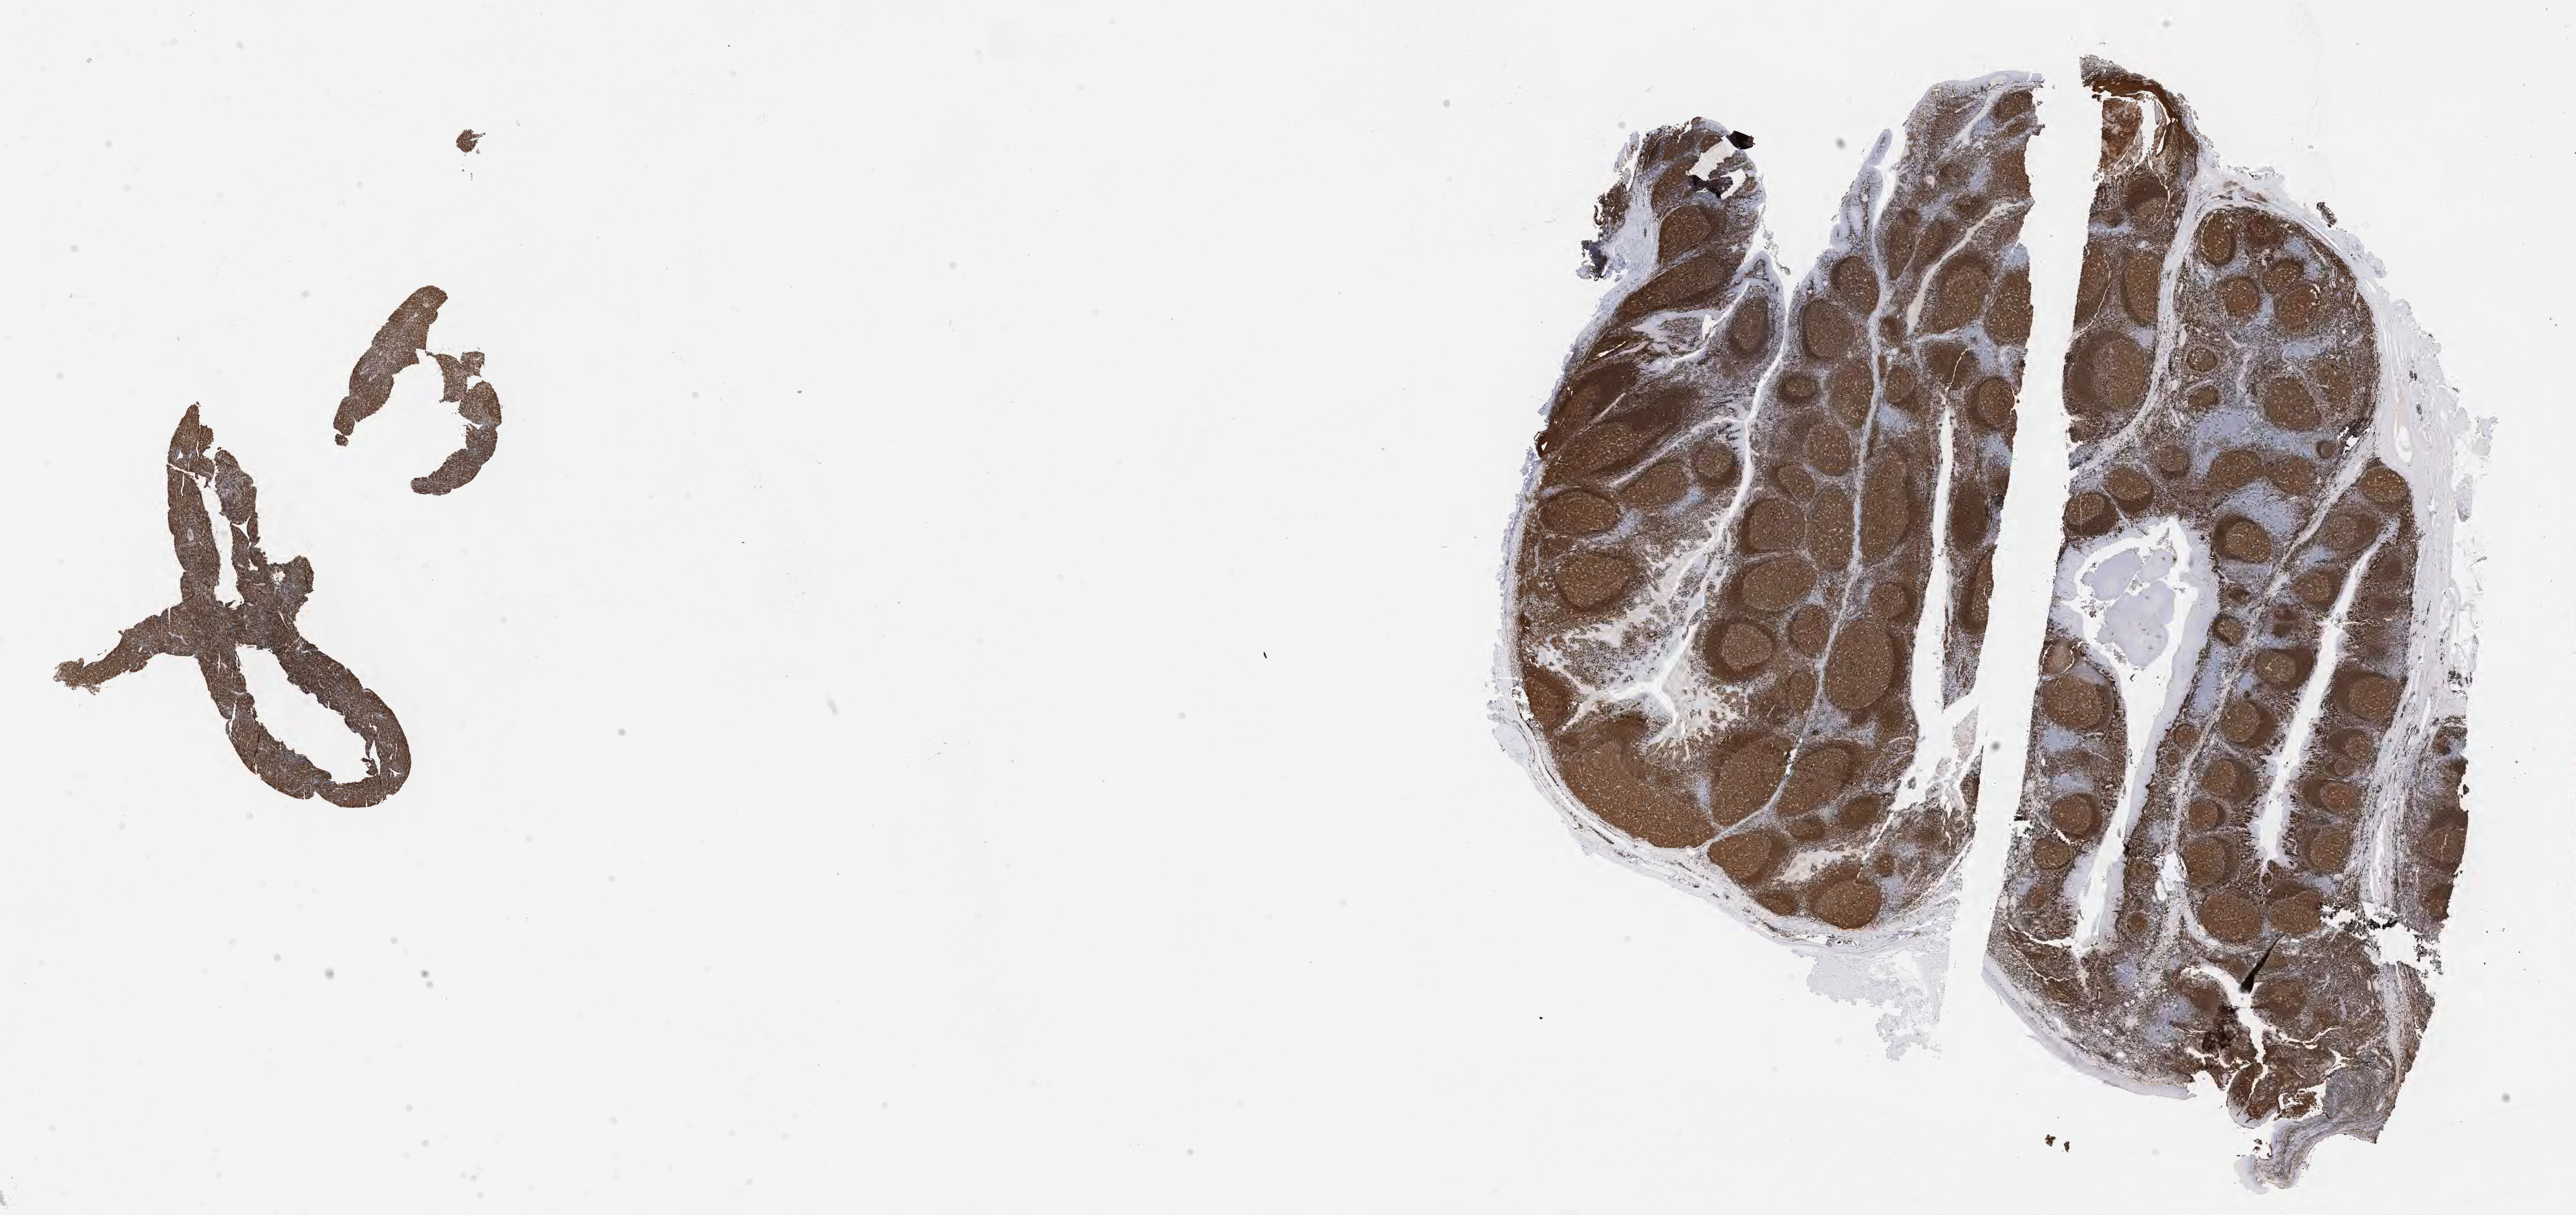
Immunohistochemistry (IHC) whole-slide image stained for CD79a, a low-resolution overview of the entire scanned area, about 32.2 x 15.2 mm. Patient: male, age 52 years.
• specimen: tumor tissue; anatomic site: liver